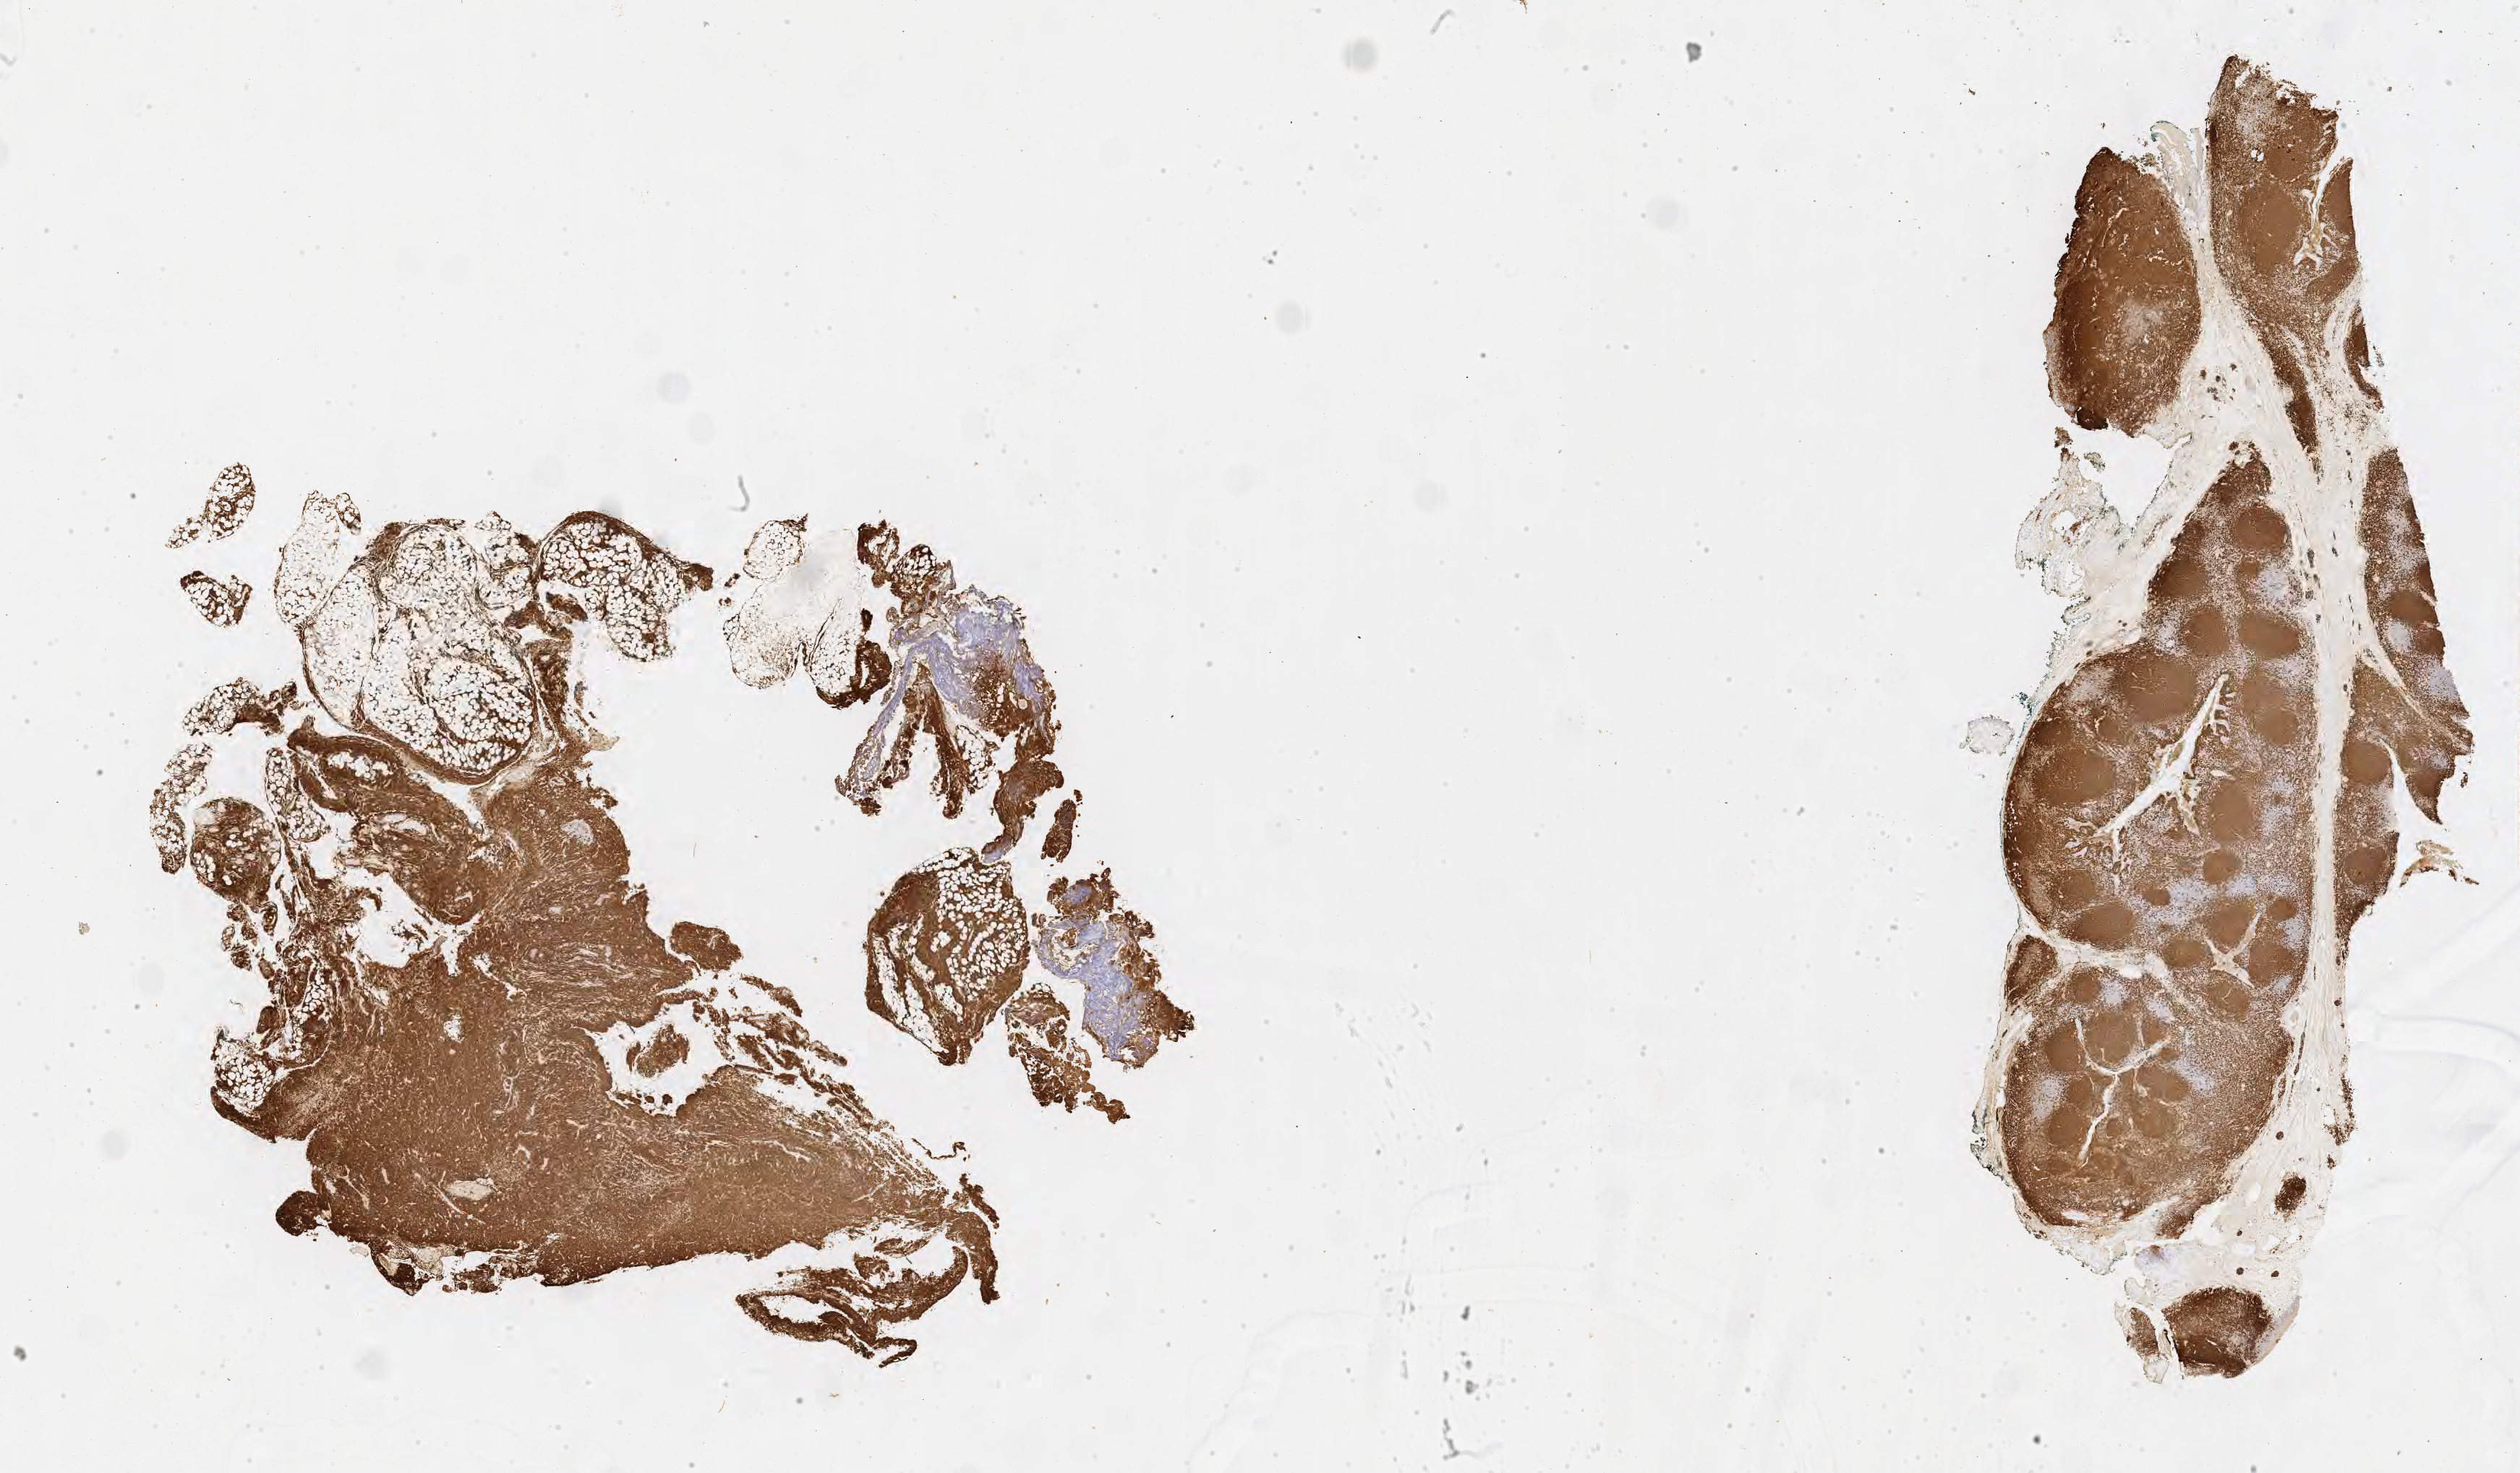
IHC for CD20, whole-slide image, shown as a low-resolution overview of the whole scanned area (about 28.2 x 16.5 mm). Specimen: tumor tissue. Anatomic site: abdominal lymph node. Male, age 9 years at initial diagnosis.
Histologic diagnosis: Burkitt lymphoma, NOS.